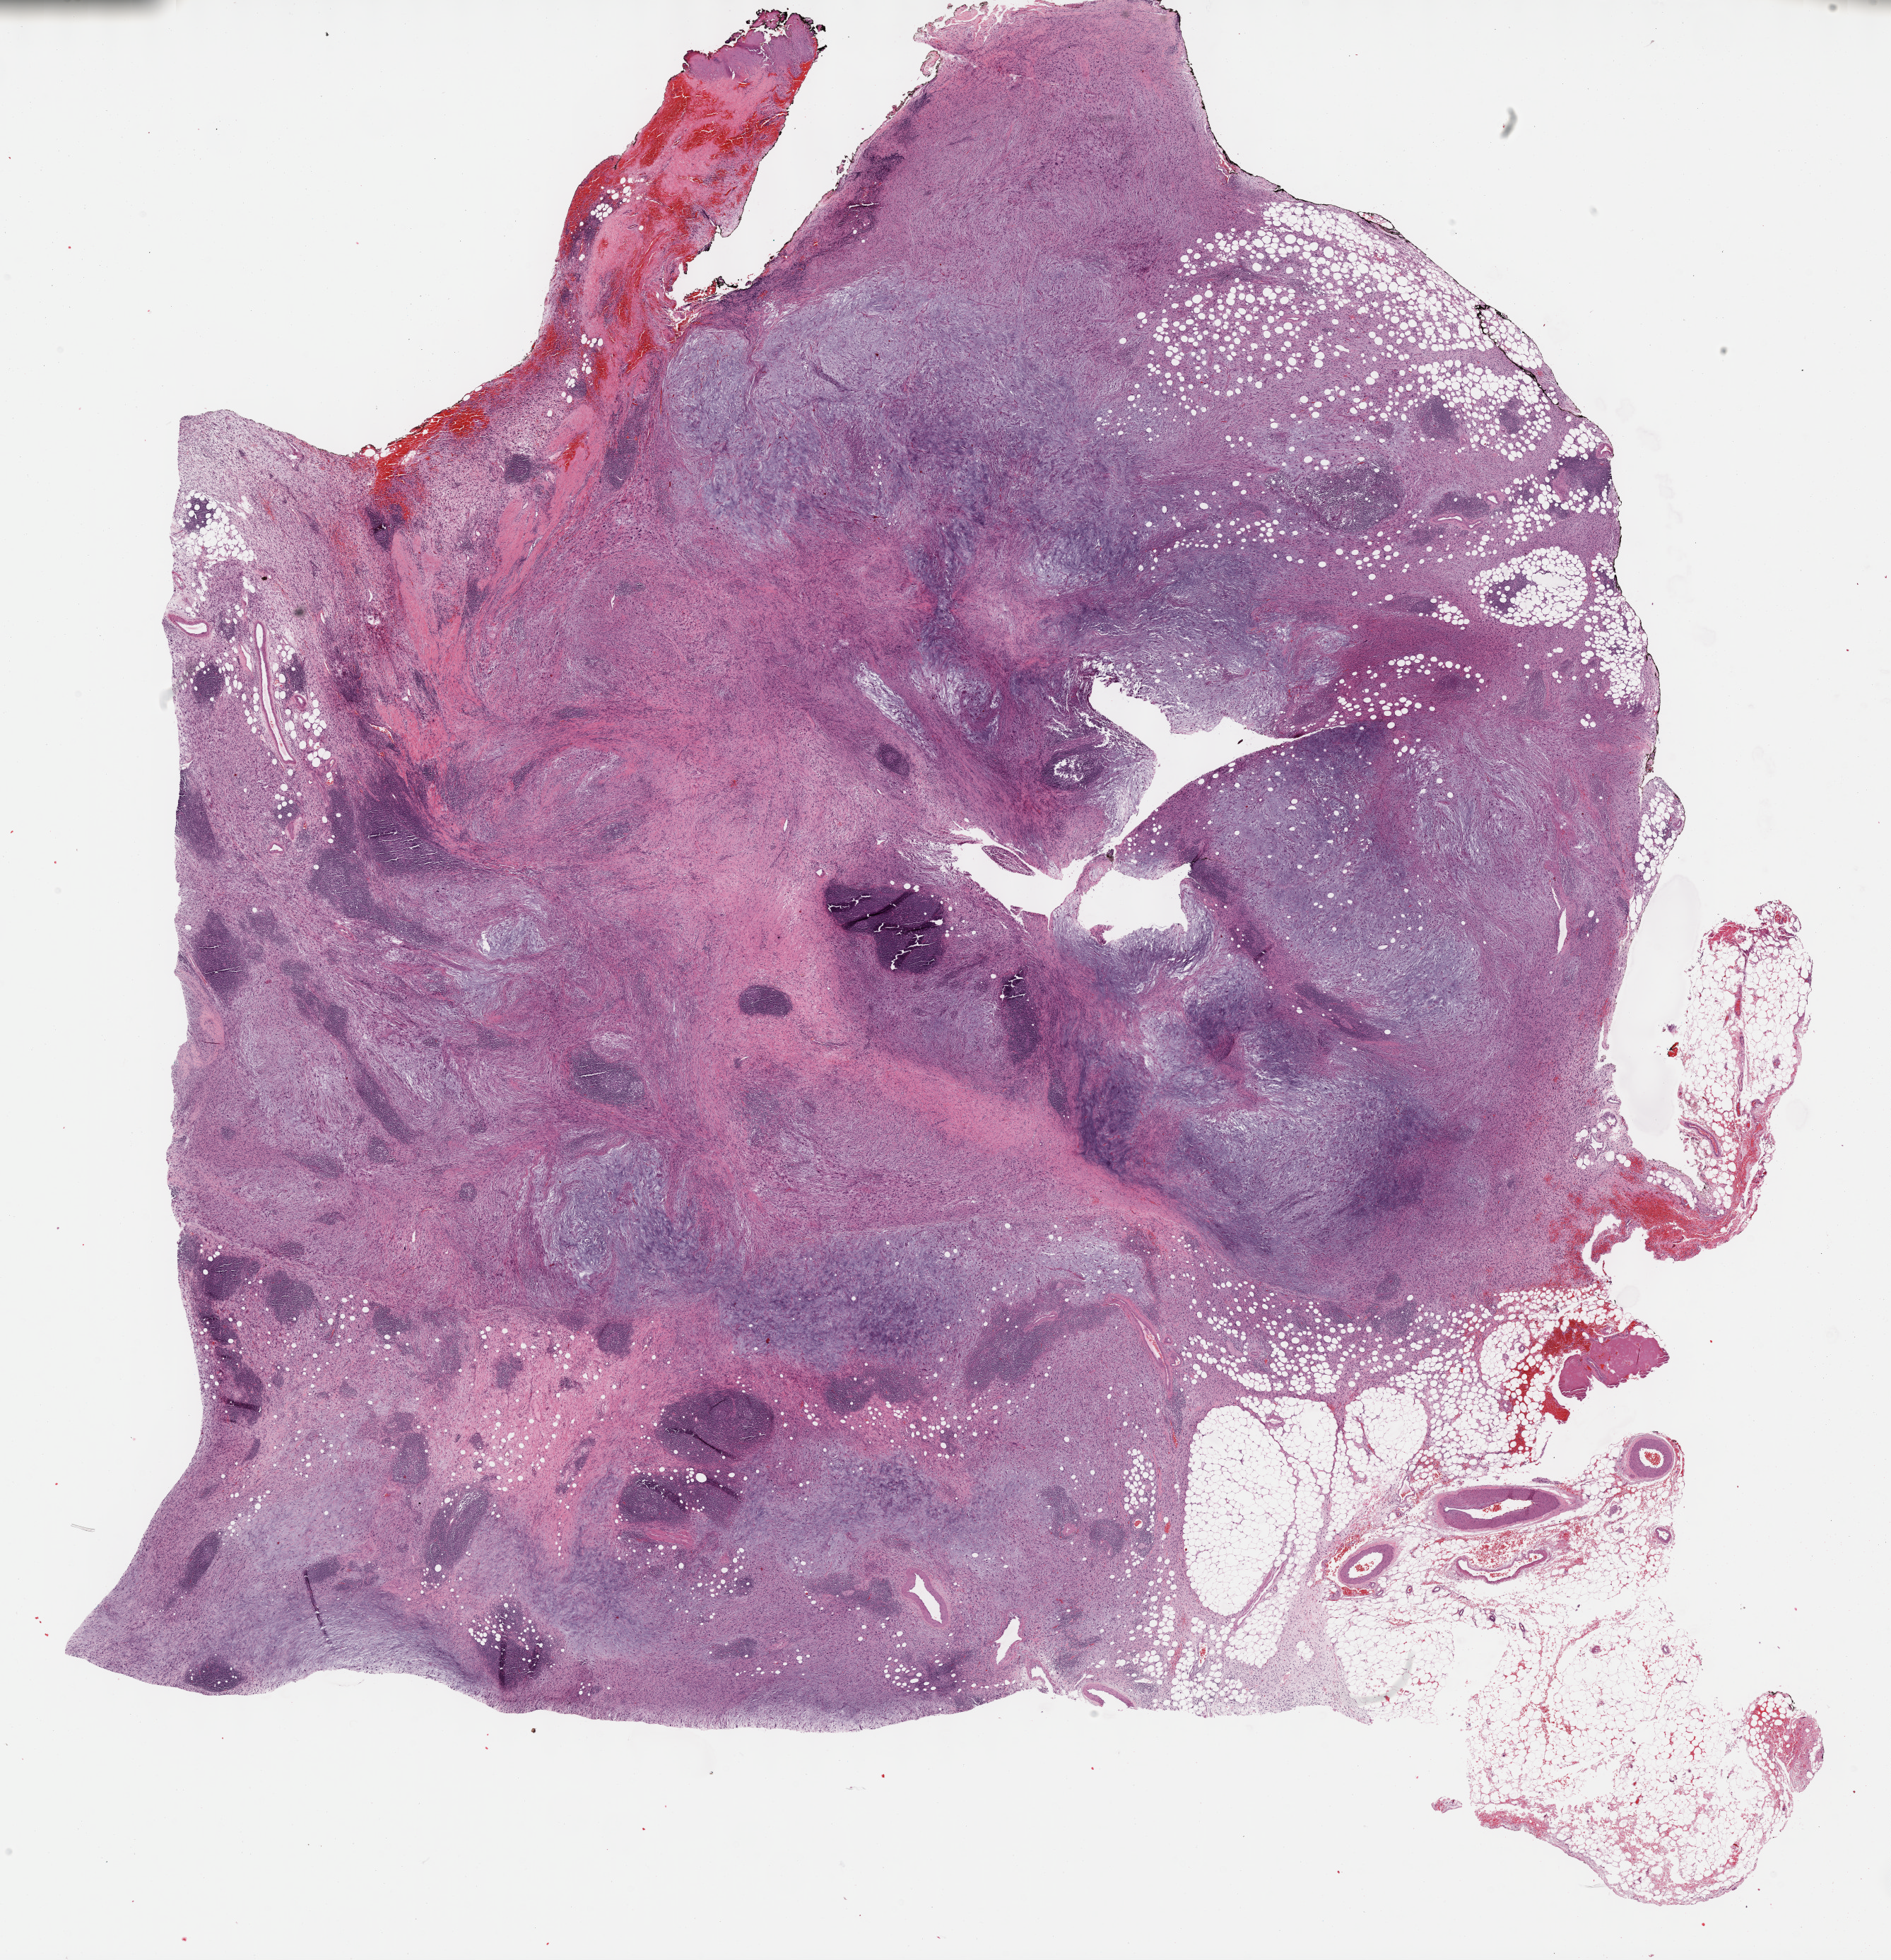
Whole-slide histology image, H&E, a low-resolution overview of the entire scanned area, about 21.6 x 22.4 mm (from a 40x scan); FFPE section; retroperitoneum and peritoneum, primary tumour sample. Male, age 60 years at initial diagnosis.
* histologic diagnosis: Dedifferentiated liposarcoma (retroperitoneum)